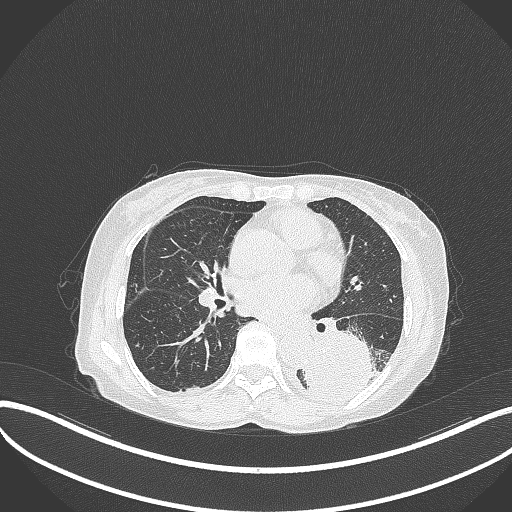
Chest CT, one axial slice. Slice 149 of 370 in the series (ordered by position). 120 kVp. Lung window (W 1500 / L -600 HU). 1 mm slice thickness. 512 × 512 image matrix. Female patient, age 78 years. Case-level facts recorded for this patient, not image findings: clinical TNM (as recorded): T3 N0 M1.
Outlined on this slice (bounding box drawn by a radiologist):
- lung tumour (recorded histology: squamous cell carcinoma): box from (x=301, y=327) to (x=387, y=405) px